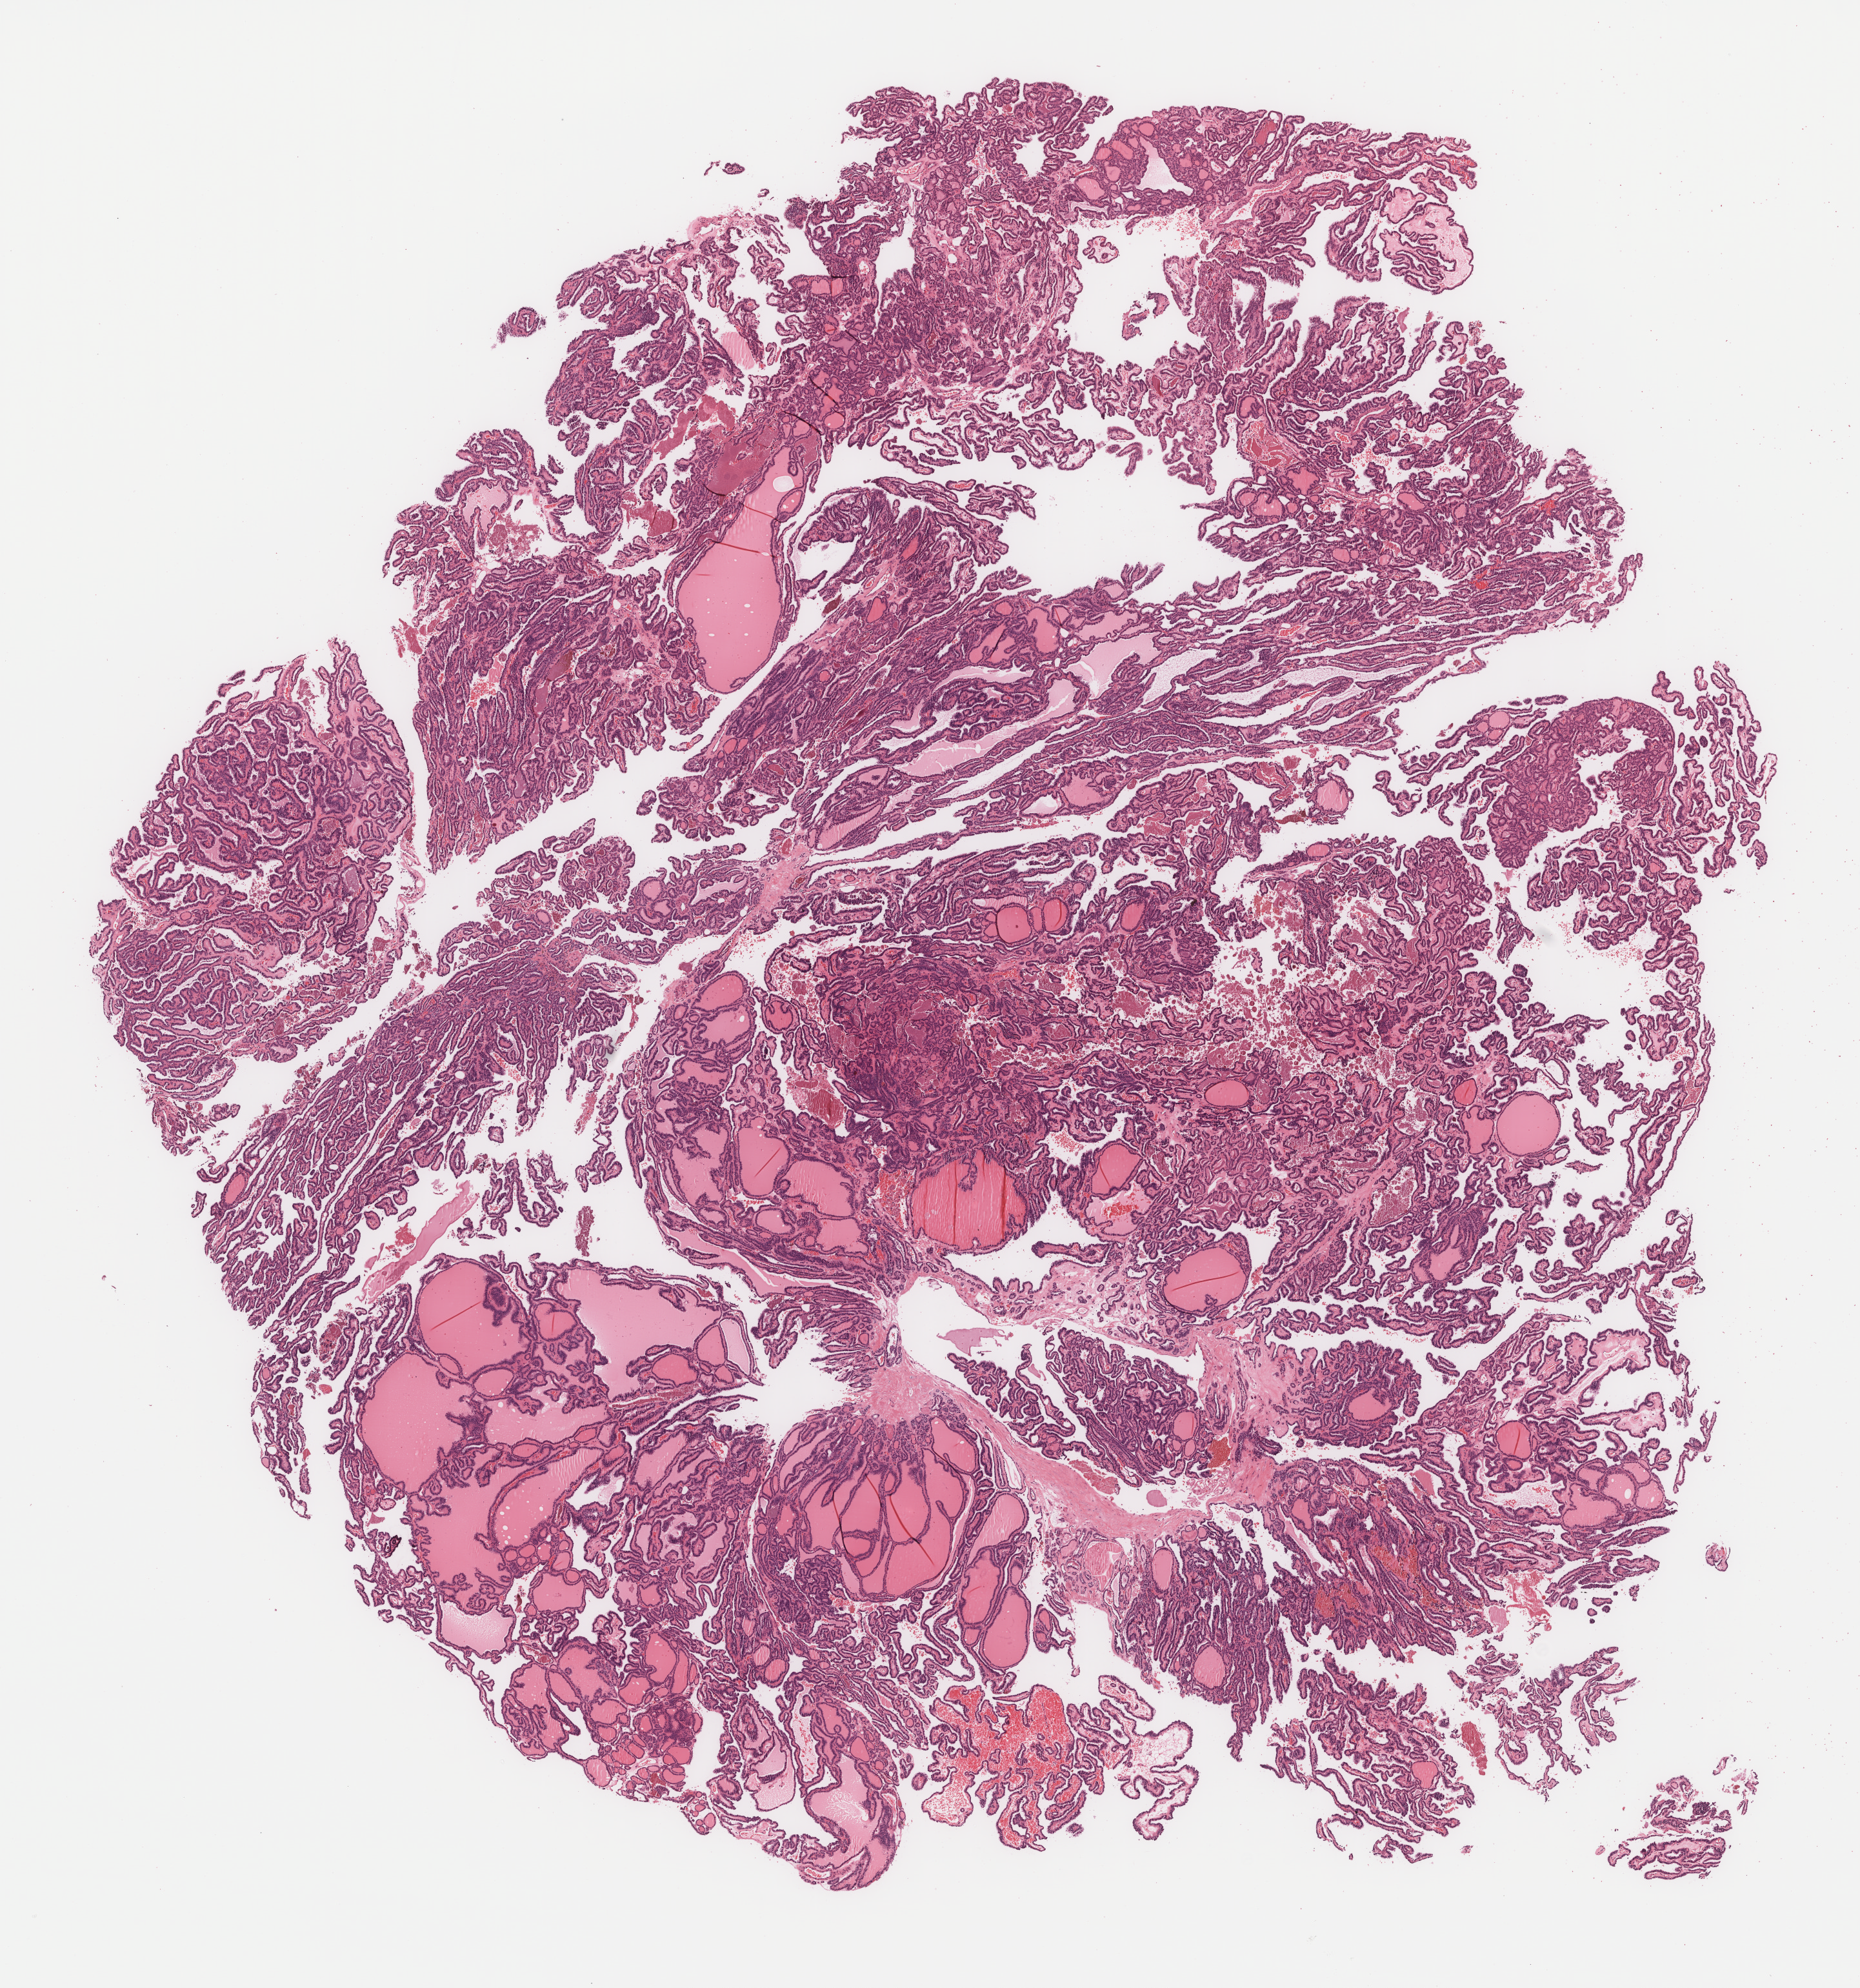
Whole-slide histology image, H&E-stained — a low-resolution overview of the entire scanned area, about 11.6 x 12.4 mm, formalin-fixed paraffin-embedded (FFPE) diagnostic section, thyroid, primary tumour sample. Patient: female, age at initial diagnosis 55 years.
AJCC pathologic stage: III. Laterality: left. Histologic diagnosis: Papillary adenocarcinoma, NOS (thyroid gland). TNM: T2 N1a MX.